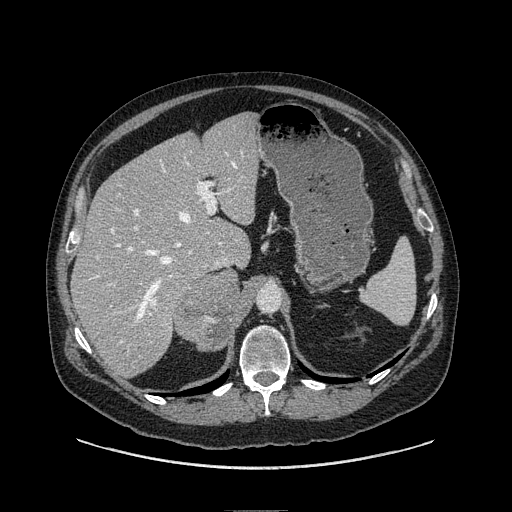
Contrast-enhanced abdominal CT, one axial slice. Slice 67 of 149 in the series (ordered by position). Soft-tissue window (W 400 / L 40 HU). 1.25 mm slice thickness. 512 × 512 image matrix, field of view 440 × 440 mm. Male patient. Case-level facts recorded for this patient, not image findings: diagnosis: adrenocortical carcinoma; tumour side: right adrenal; tumour size at pathology: 7.5 cm.
Structures marked on this image (semi-automatic segmentation, software-assisted and operator-edited):
- mass: bounding box [x1, y1, x2, y2] px = [175, 270, 241, 350]